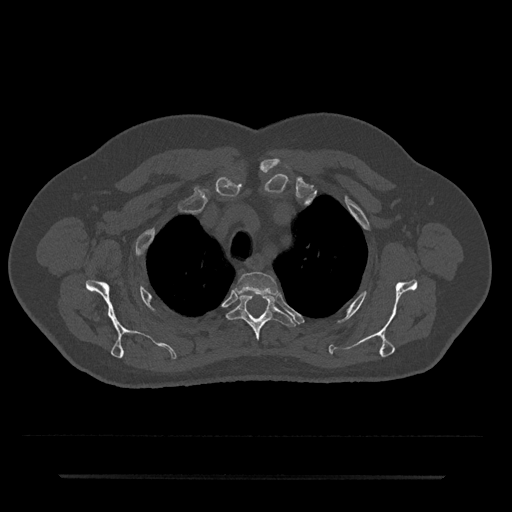
CT including the spine, one axial slice; position 576 of 797 along the scan axis; bone window (W 1800 / L 400 HU); 0.5 mm slice thickness; 512 × 512 image matrix. Patient: male, 69 years. From the clinical record (not read from this slice): primary cancer: prostate.
Outlined on this slice (semi-automatic segmentation, software-assisted and operator-edited):
- T2 vertebra: bounding box [x1, y1, x2, y2] px = [236, 272, 278, 295]
- T3 vertebra: [226, 294, 297, 340]